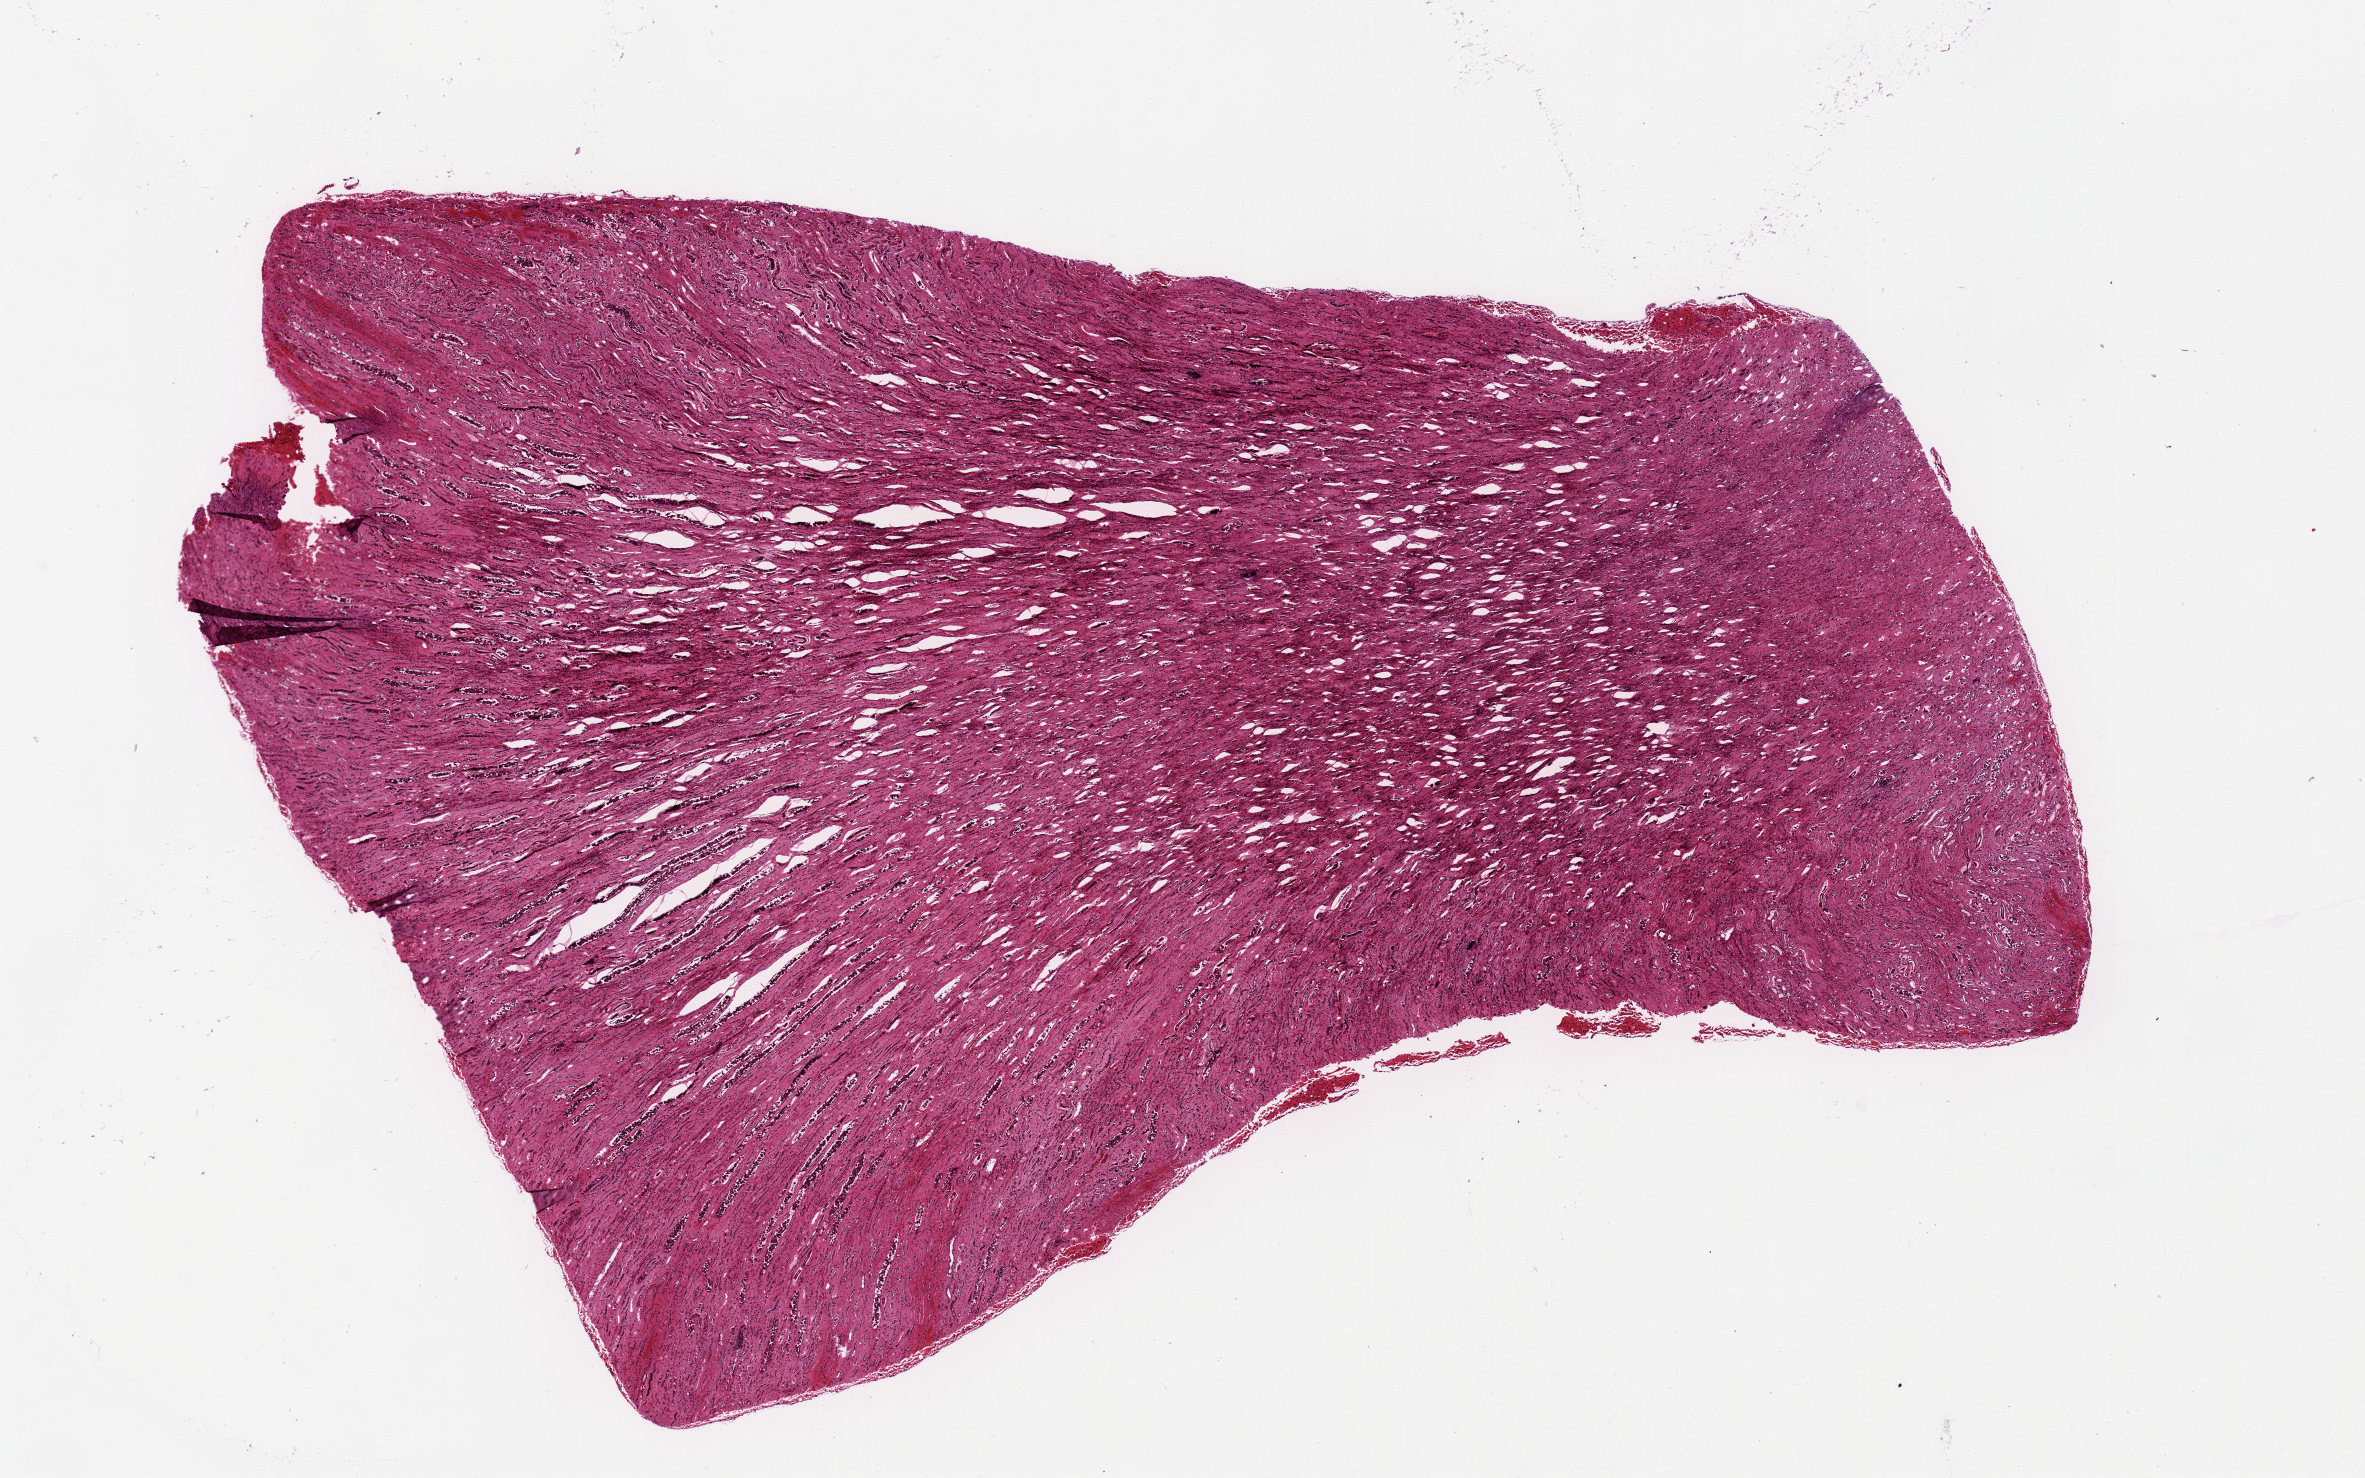
Whole-slide image, H&E stain, brightfield, low-resolution overview of the scanned area, about 18.7 x 11.7 mm, PAXgene-fixed, paraffin-embedded tissue, target tissue: renal medulla, donor tissue sample. Donor sex: male.
Review note (as recorded): Moderate-severe autolysis of tubules. Moderate interstitial fibrosis.